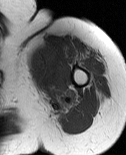
MRI of an extremity soft-tissue mass, one axial slice. Position 60 of 86 along the scan axis. MR volume resampled by the dataset authors to the PET/CT grid (not the native acquisition matrix). 3.27 mm slice thickness. 126 × 155 image matrix, field of view 123 × 151 mm. Female patient. From the clinical record (not read from this slice): histological type: pleiomorphic leiomyosarcoma; grade: high; site of the primary tumour: left biceps.
Structures marked on this image (expert contour drawn on MRI and transferred to this co-registered scan by the dataset authors):
- gross tumour volume including surrounding oedema: bounding box <27,44,67,100> (left, top, right, bottom; pixels)
- gross tumour volume (mass): <27,44,67,89>